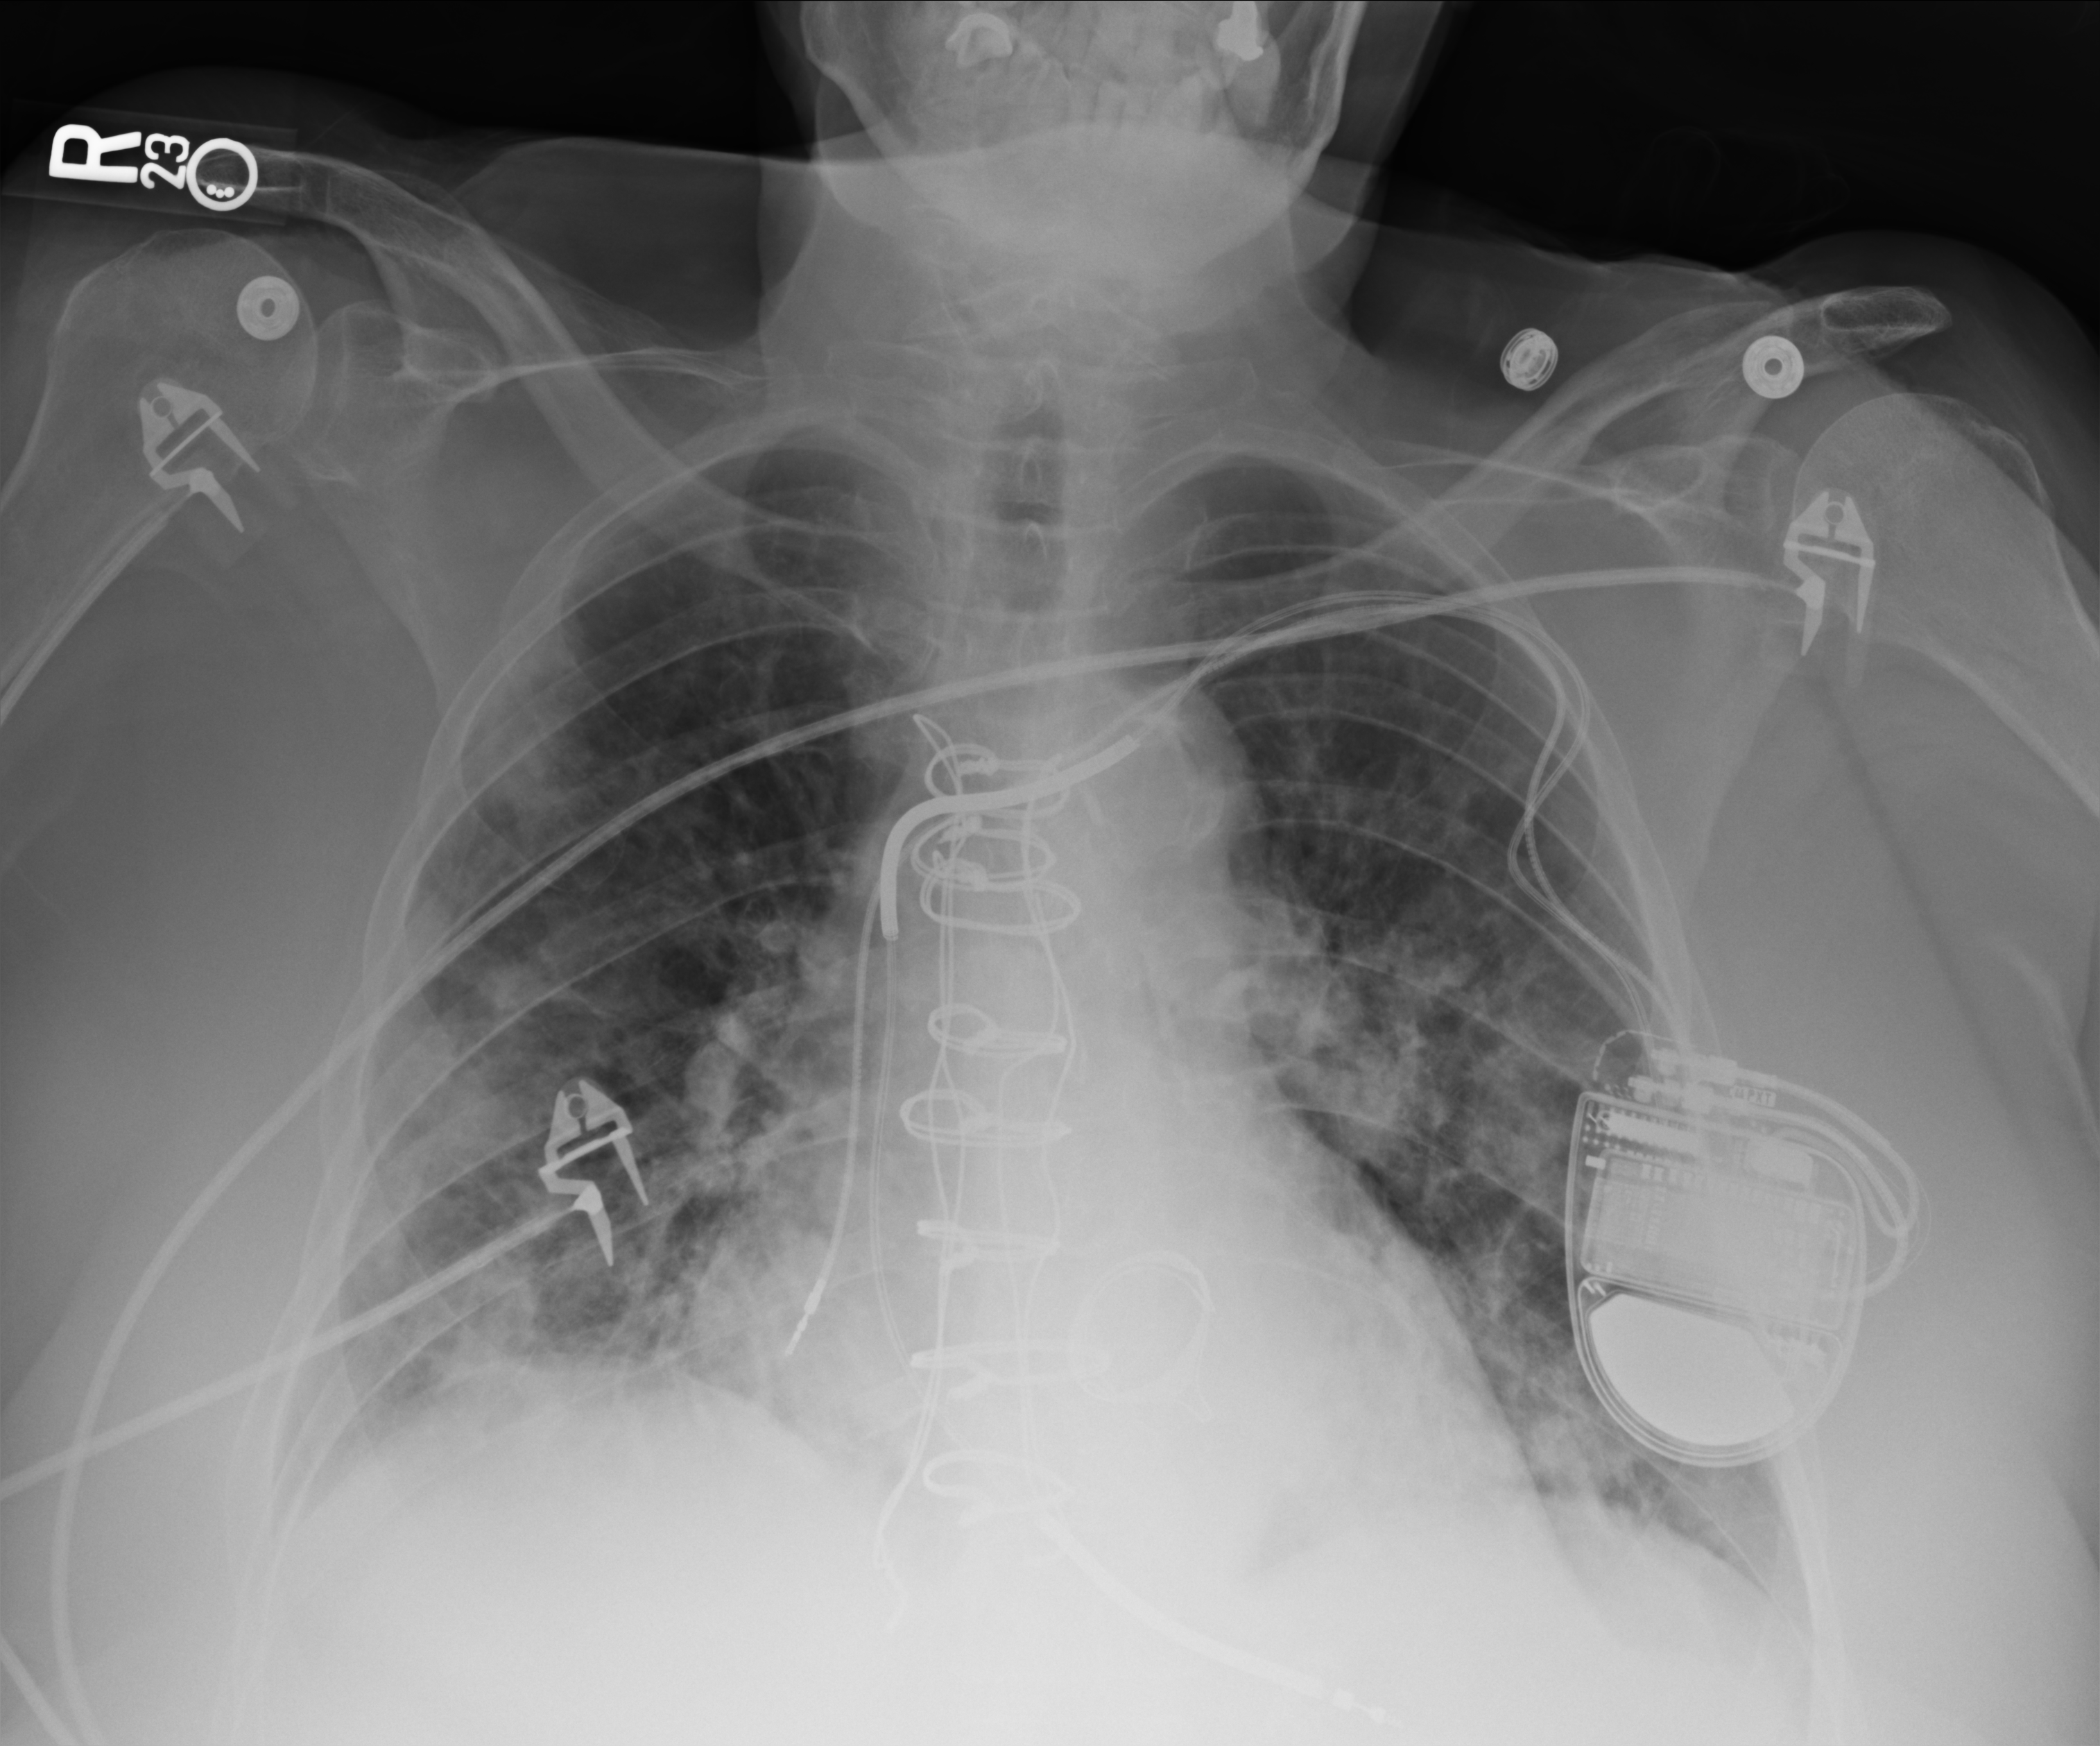
Bedside chest radiograph (computed radiography). Patient hospitalised with COVID-19; female, aged 60–74 years.
From the hospital-stay record, not from the radiograph (when in the stay this image was taken is not recorded): mechanically ventilated during this hospital stay: no; admitted to intensive care during this hospital stay: yes.